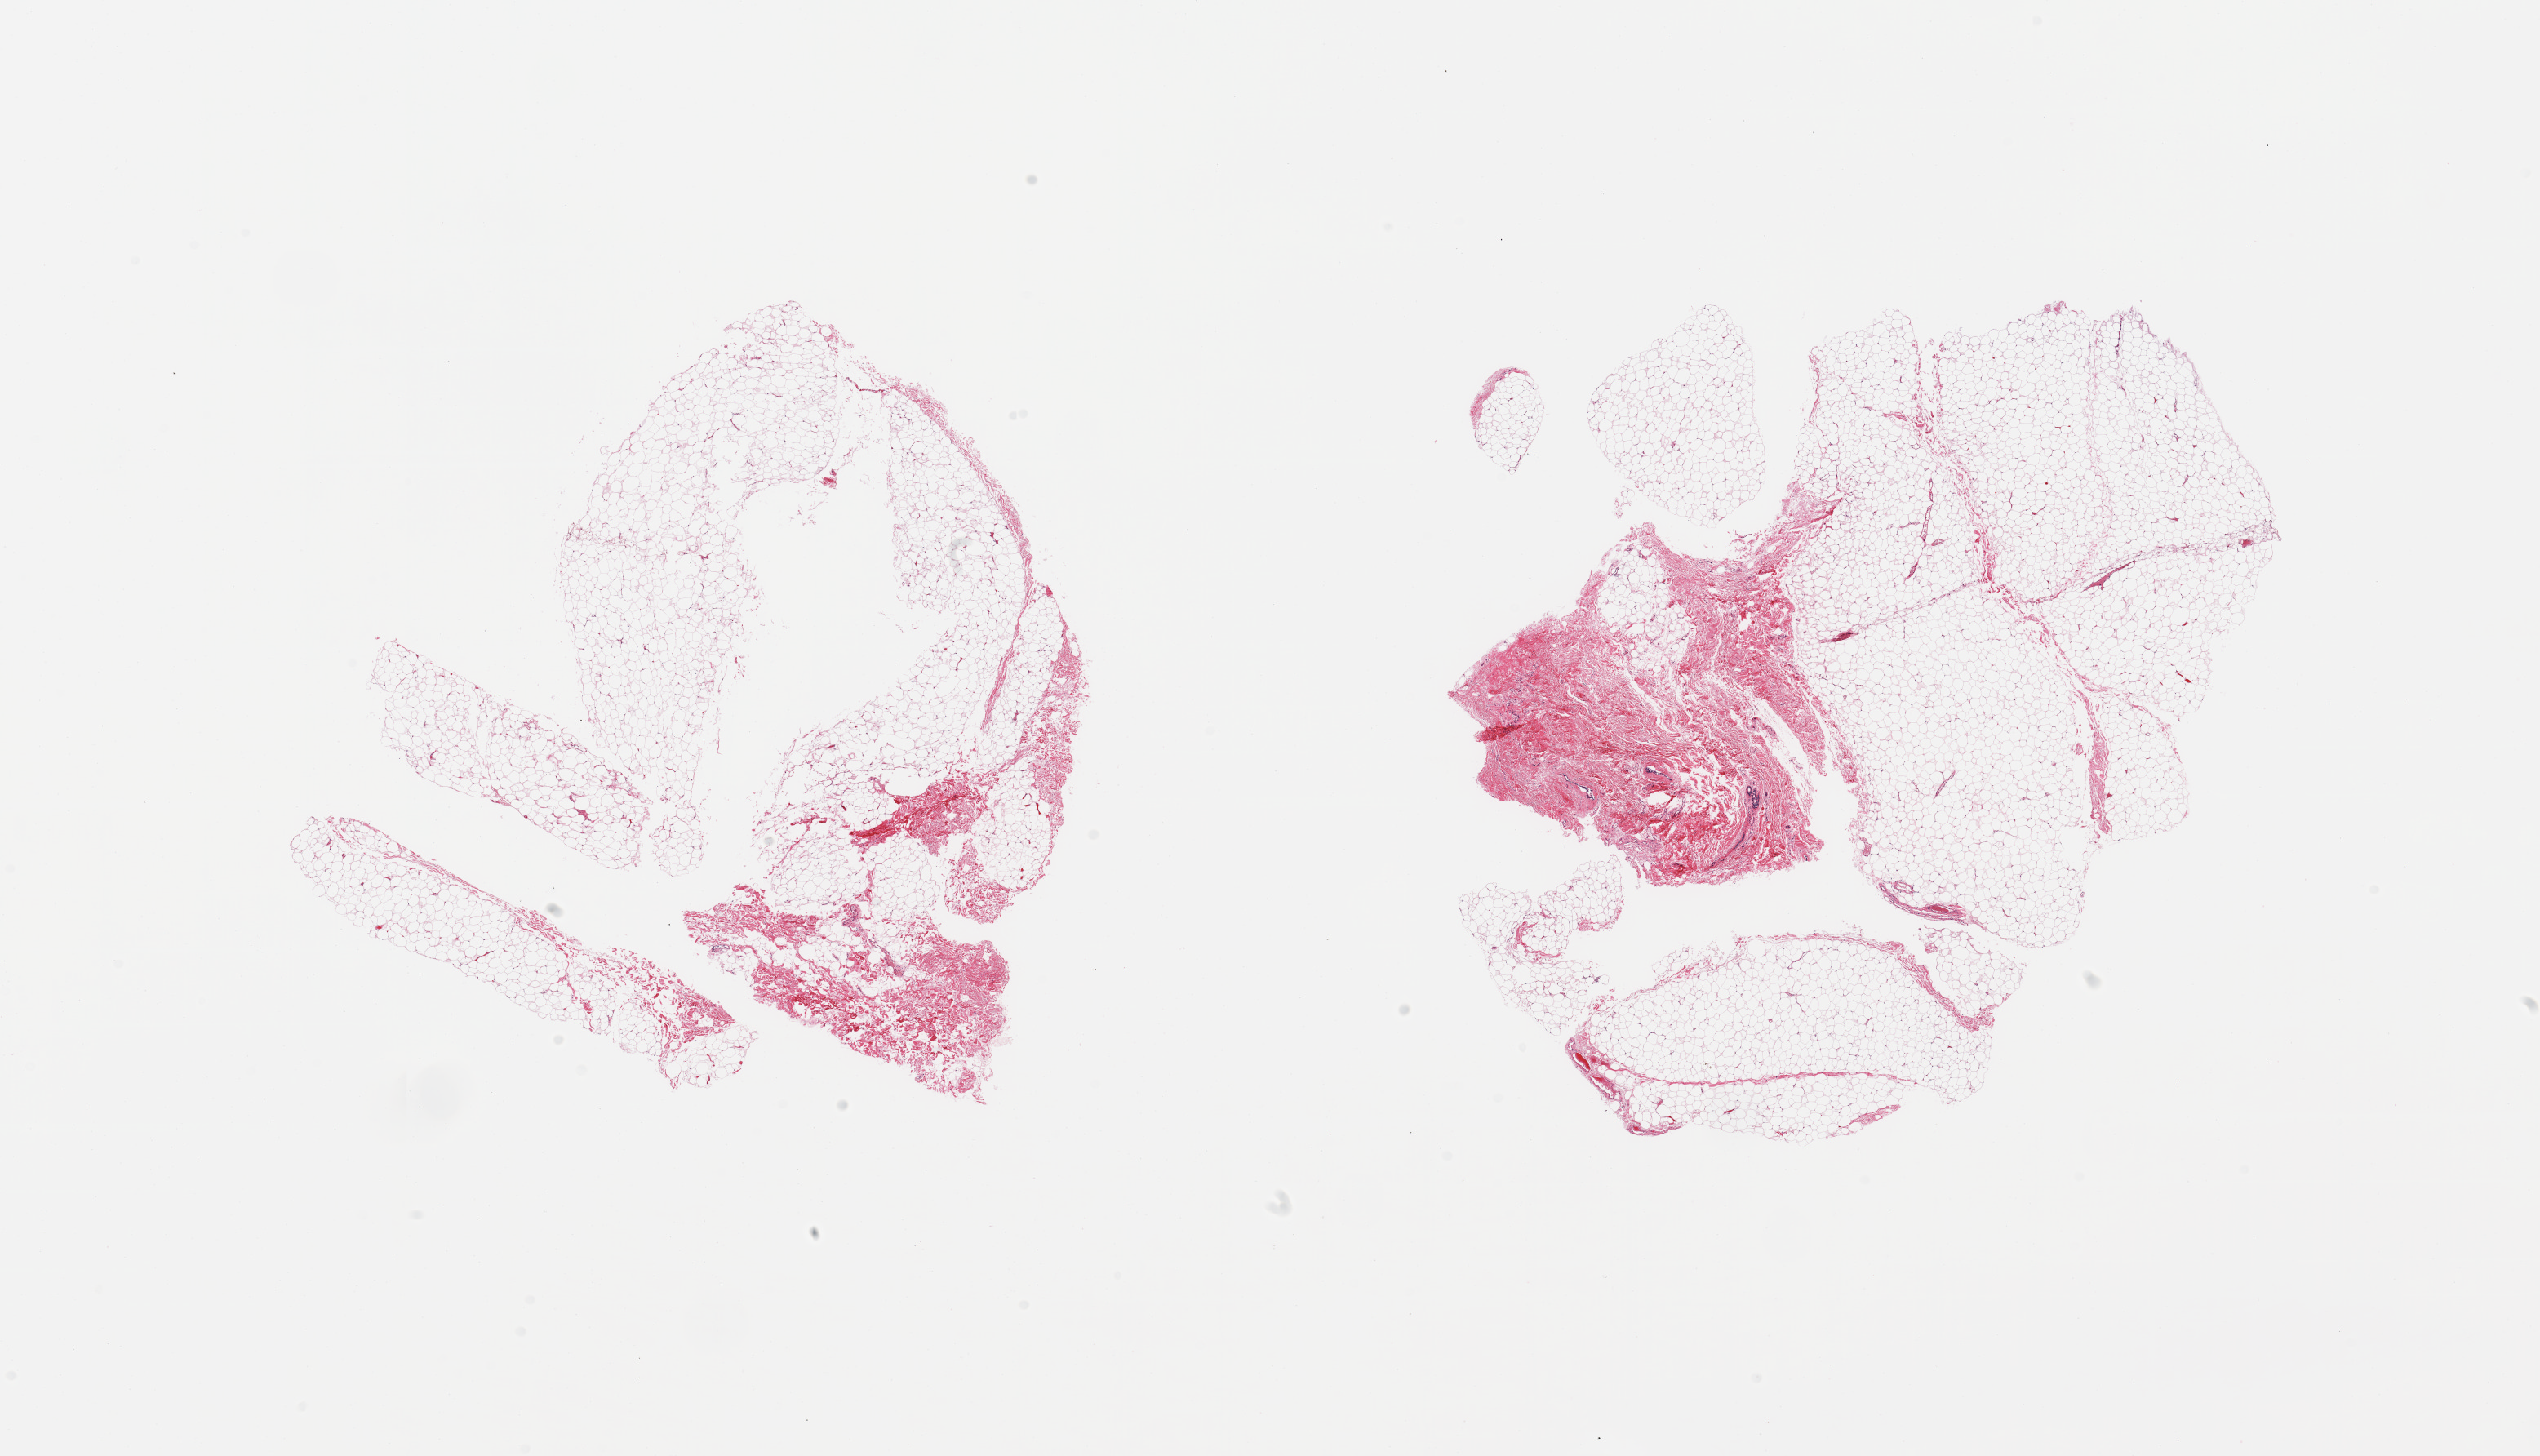
Whole-slide image, hematoxylin and eosin (H&E) stain, brightfield — a low-resolution overview of the entire scanned area, about 24.6 x 14.1 mm (from a 20x scan). PAXgene-fixed paraffin-embedded (PFPE) section. Sampled site (target tissue): breast. Donor tissue sample. Donor: male.
• review note (as recorded): 2 pieces, mainly fibroadipose elements, trace ducts